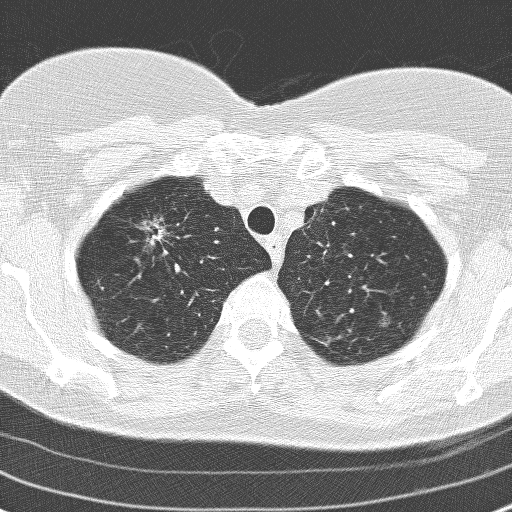
Axial slice from a low-dose chest CT screening exam, second screening round (one year after baseline), lung window (W 1500 / L -600 HU), 3.2 mm slice thickness, lung (sharp) reconstruction kernel (D), slice 30 of 160 in the series. Female, age 60 years at enrolment. Former smoker at enrolment.
Expert-annotated lung lesion, box from (x=127, y=206) to (x=181, y=257) px. Screening reader's record for this exam (one nodule recorded; not confirmed to be the boxed lesion): non-calcified nodule or mass ≥4 mm, right upper lobe, 17 × 15 mm, spiculated (stellate) margins, soft tissue attenuation, pre-existing on the prior screen: yes; interval growth: yes. Official screen result: positive, other. Lung cancer was diagnosed 78 days after this screen: adenocarcinoma, NOS, right upper lobe, moderately differentiated (G2), stage IA (AJCC 6th edition), 23 mm at pathology.